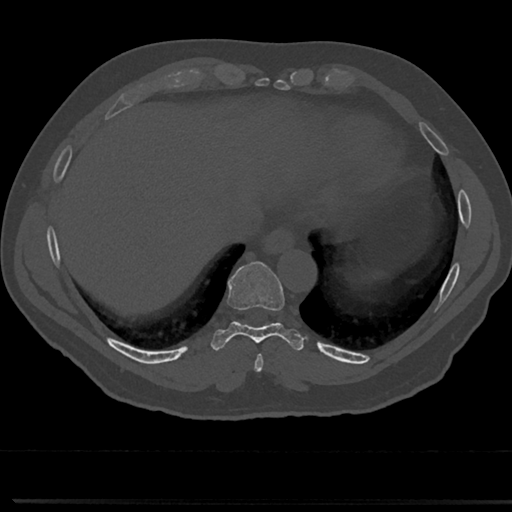
CT including the spine, one axial slice. Slice 302 of 817 in the series (ordered by position). Reconstruction kernel Br40s/3. 120 kVp. Bone window (W 1800 / L 400 HU). 0.5 mm slice thickness. 512 × 512 image matrix. Patient: male, 61 years. From the clinical record (not read from this slice): primary cancer: prostate.
Annotated regions visible in this slice (semi-automatically segmented with operator editing):
- T8 vertebra: bounding box <234,306,285,356> (left, top, right, bottom; pixels)
- T9 vertebra: <232,266,283,330>